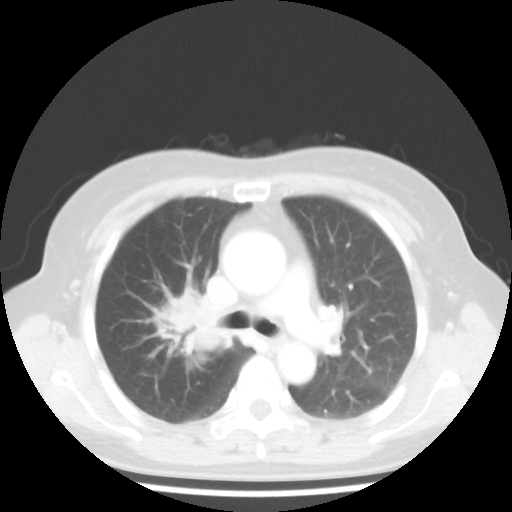
Chest CT, one axial slice; reconstruction kernel STANDARD; 100 kVp; lung window (W 1500 / L -600 HU); 5 mm slice thickness; 512 × 512 image matrix, field of view 316 × 316 mm. Patient: female, 62 years. Case-level facts recorded for this patient, not image findings: clinical TNM (as recorded): T3 N0 M0; histopathological grade: G3.
Structures marked on this image (bounding box drawn by a radiologist):
- lung tumour (recorded histology: small cell carcinoma): bounding box [x1, y1, x2, y2] px = [154, 285, 235, 371]